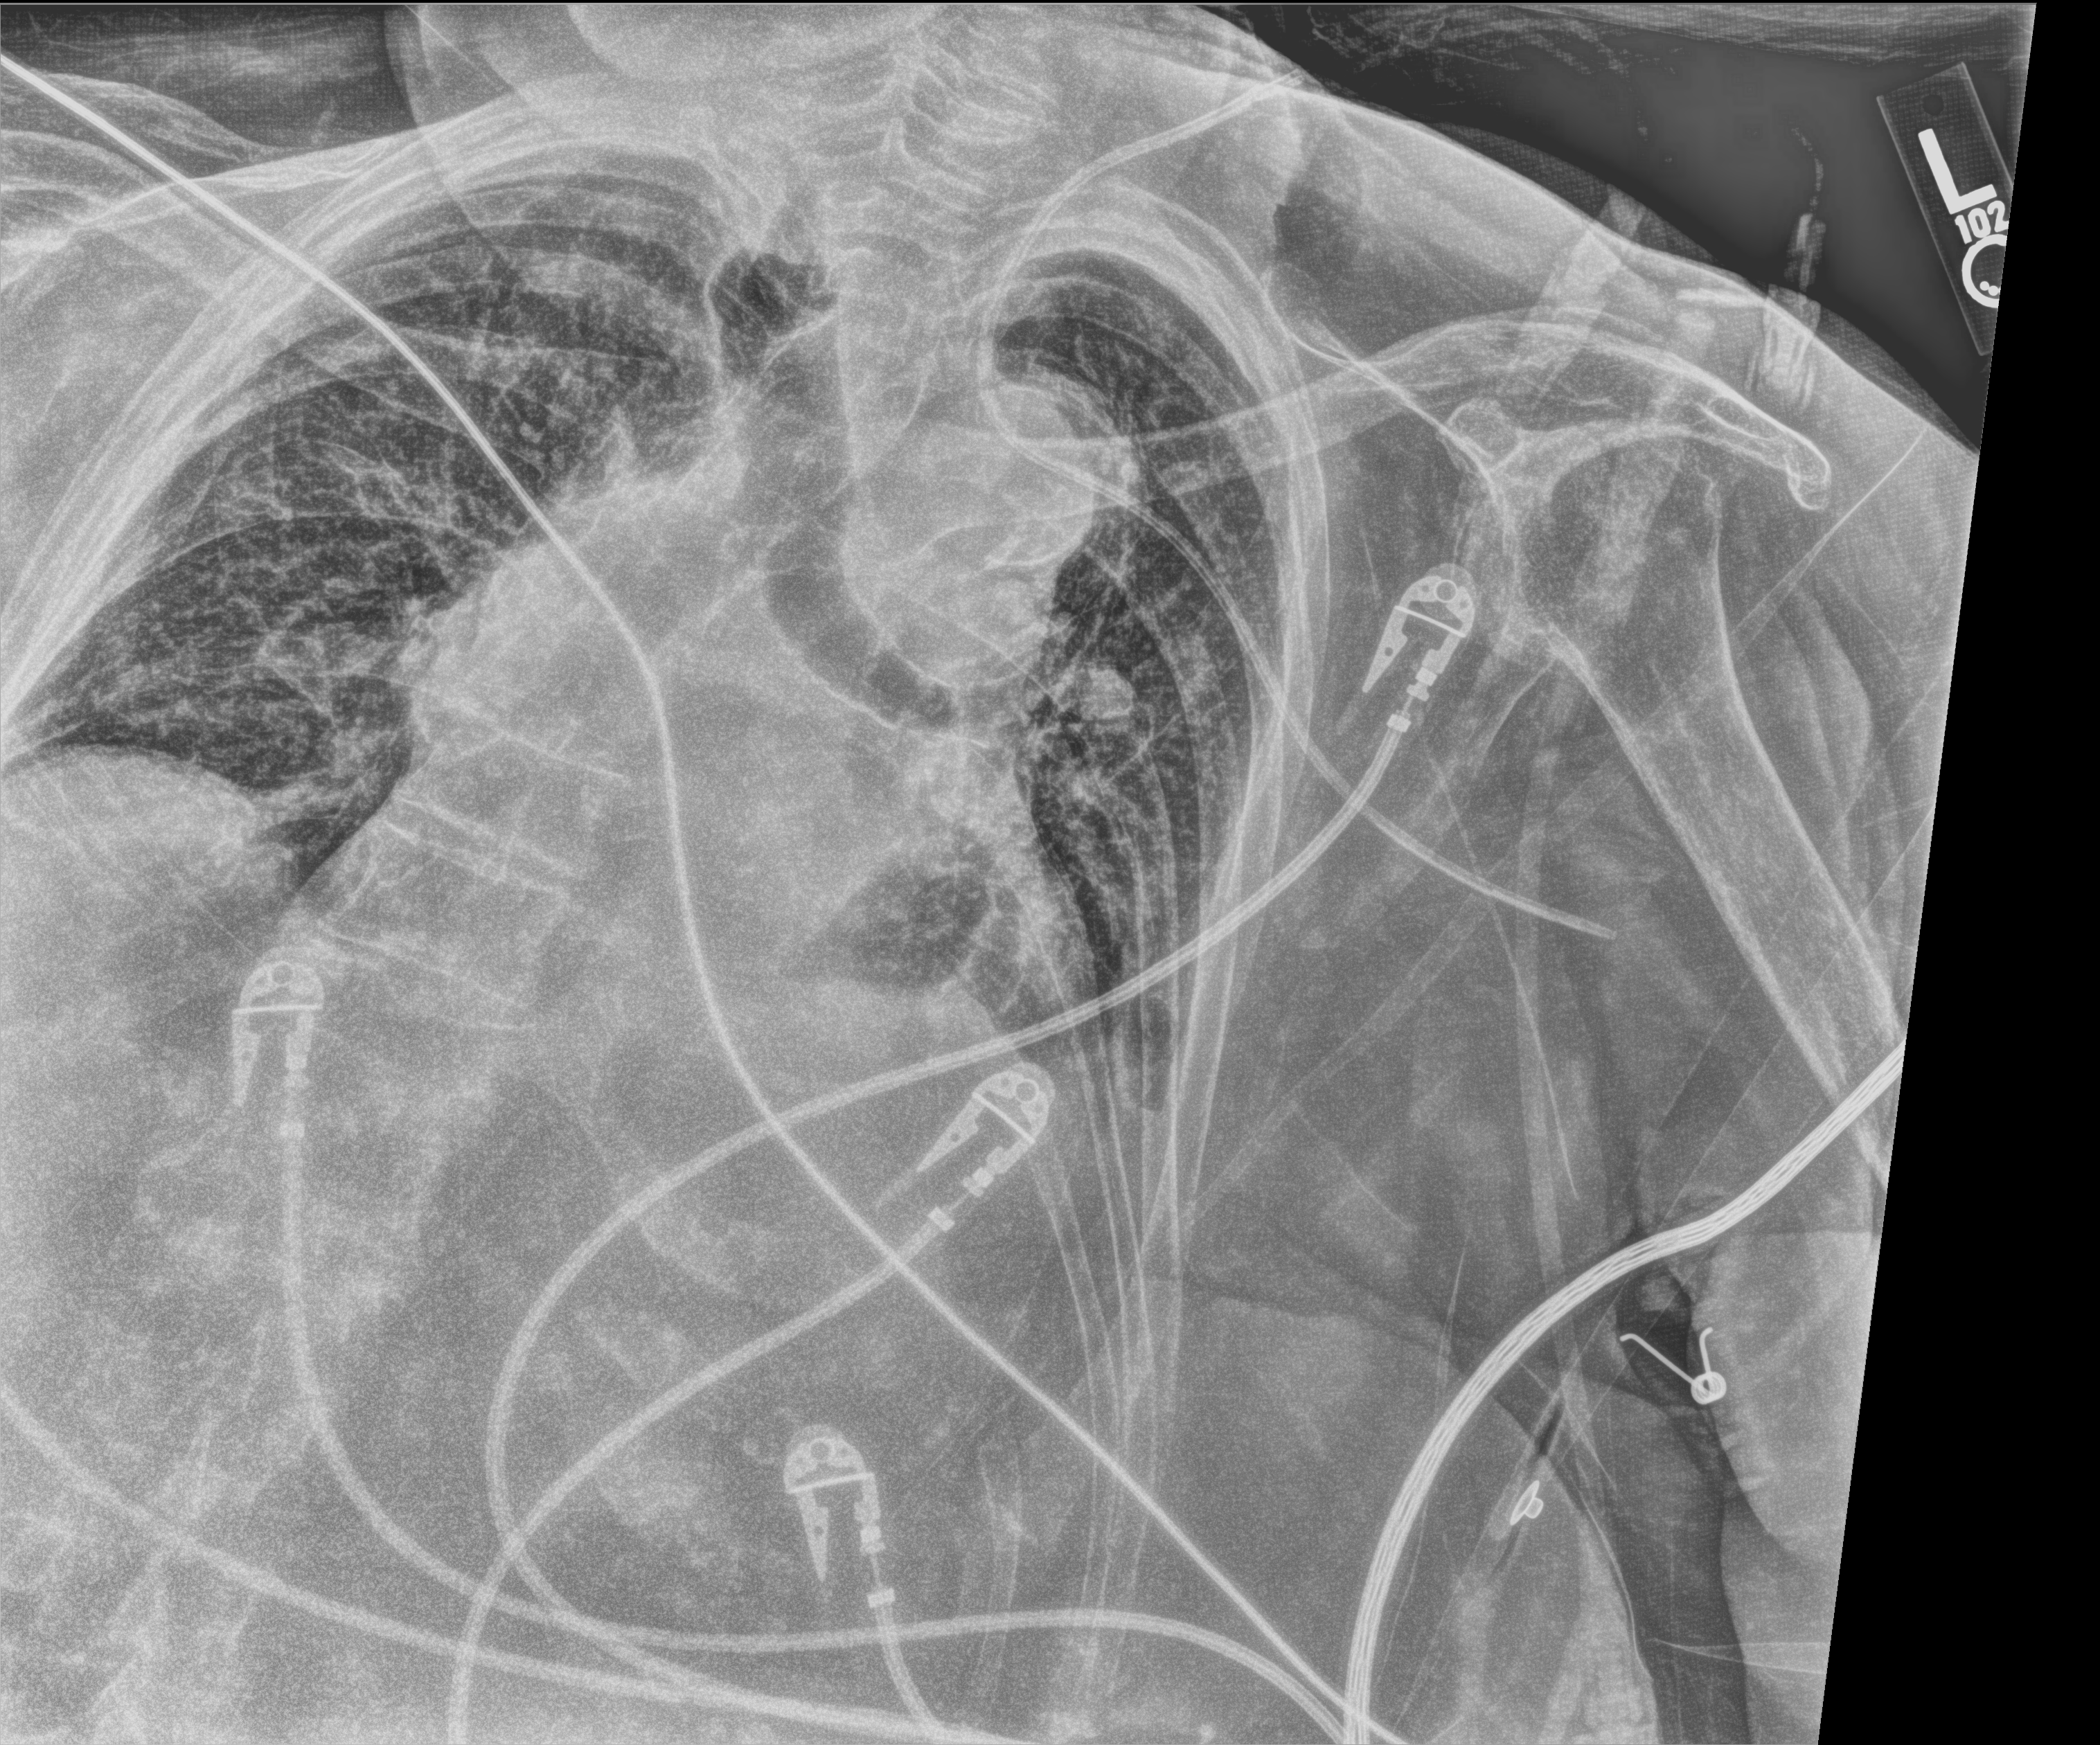
Portable chest radiograph, anteroposterior (AP) projection. Female patient hospitalised with COVID-19, age 75–90 years.
From the hospital-stay record, not from the radiograph (when in the stay this image was taken is not recorded):
- admitted to intensive care during this hospital stay: yes
- mechanically ventilated during this hospital stay: no